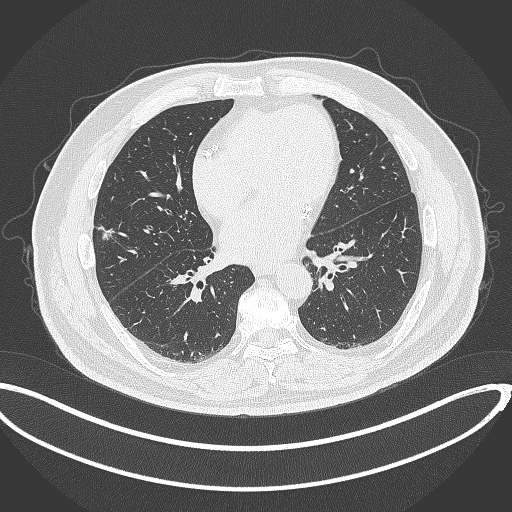
Chest CT, one axial slice; slice 140 of 340 in the series (ordered by position); 120 kVp; lung window (W 1500 / L -600 HU); 1 mm slice thickness; 512 × 512 image matrix, field of view 427 × 427 mm. Patient: male, 68 years. Case-level facts recorded for this patient, not image findings: clinical TNM (as recorded): T1c N0 M0.
Outlined on this slice (bounding box drawn by a radiologist):
- lung tumour (recorded histology: adenocarcinoma): bounding box <98,224,117,241> (left, top, right, bottom; pixels)